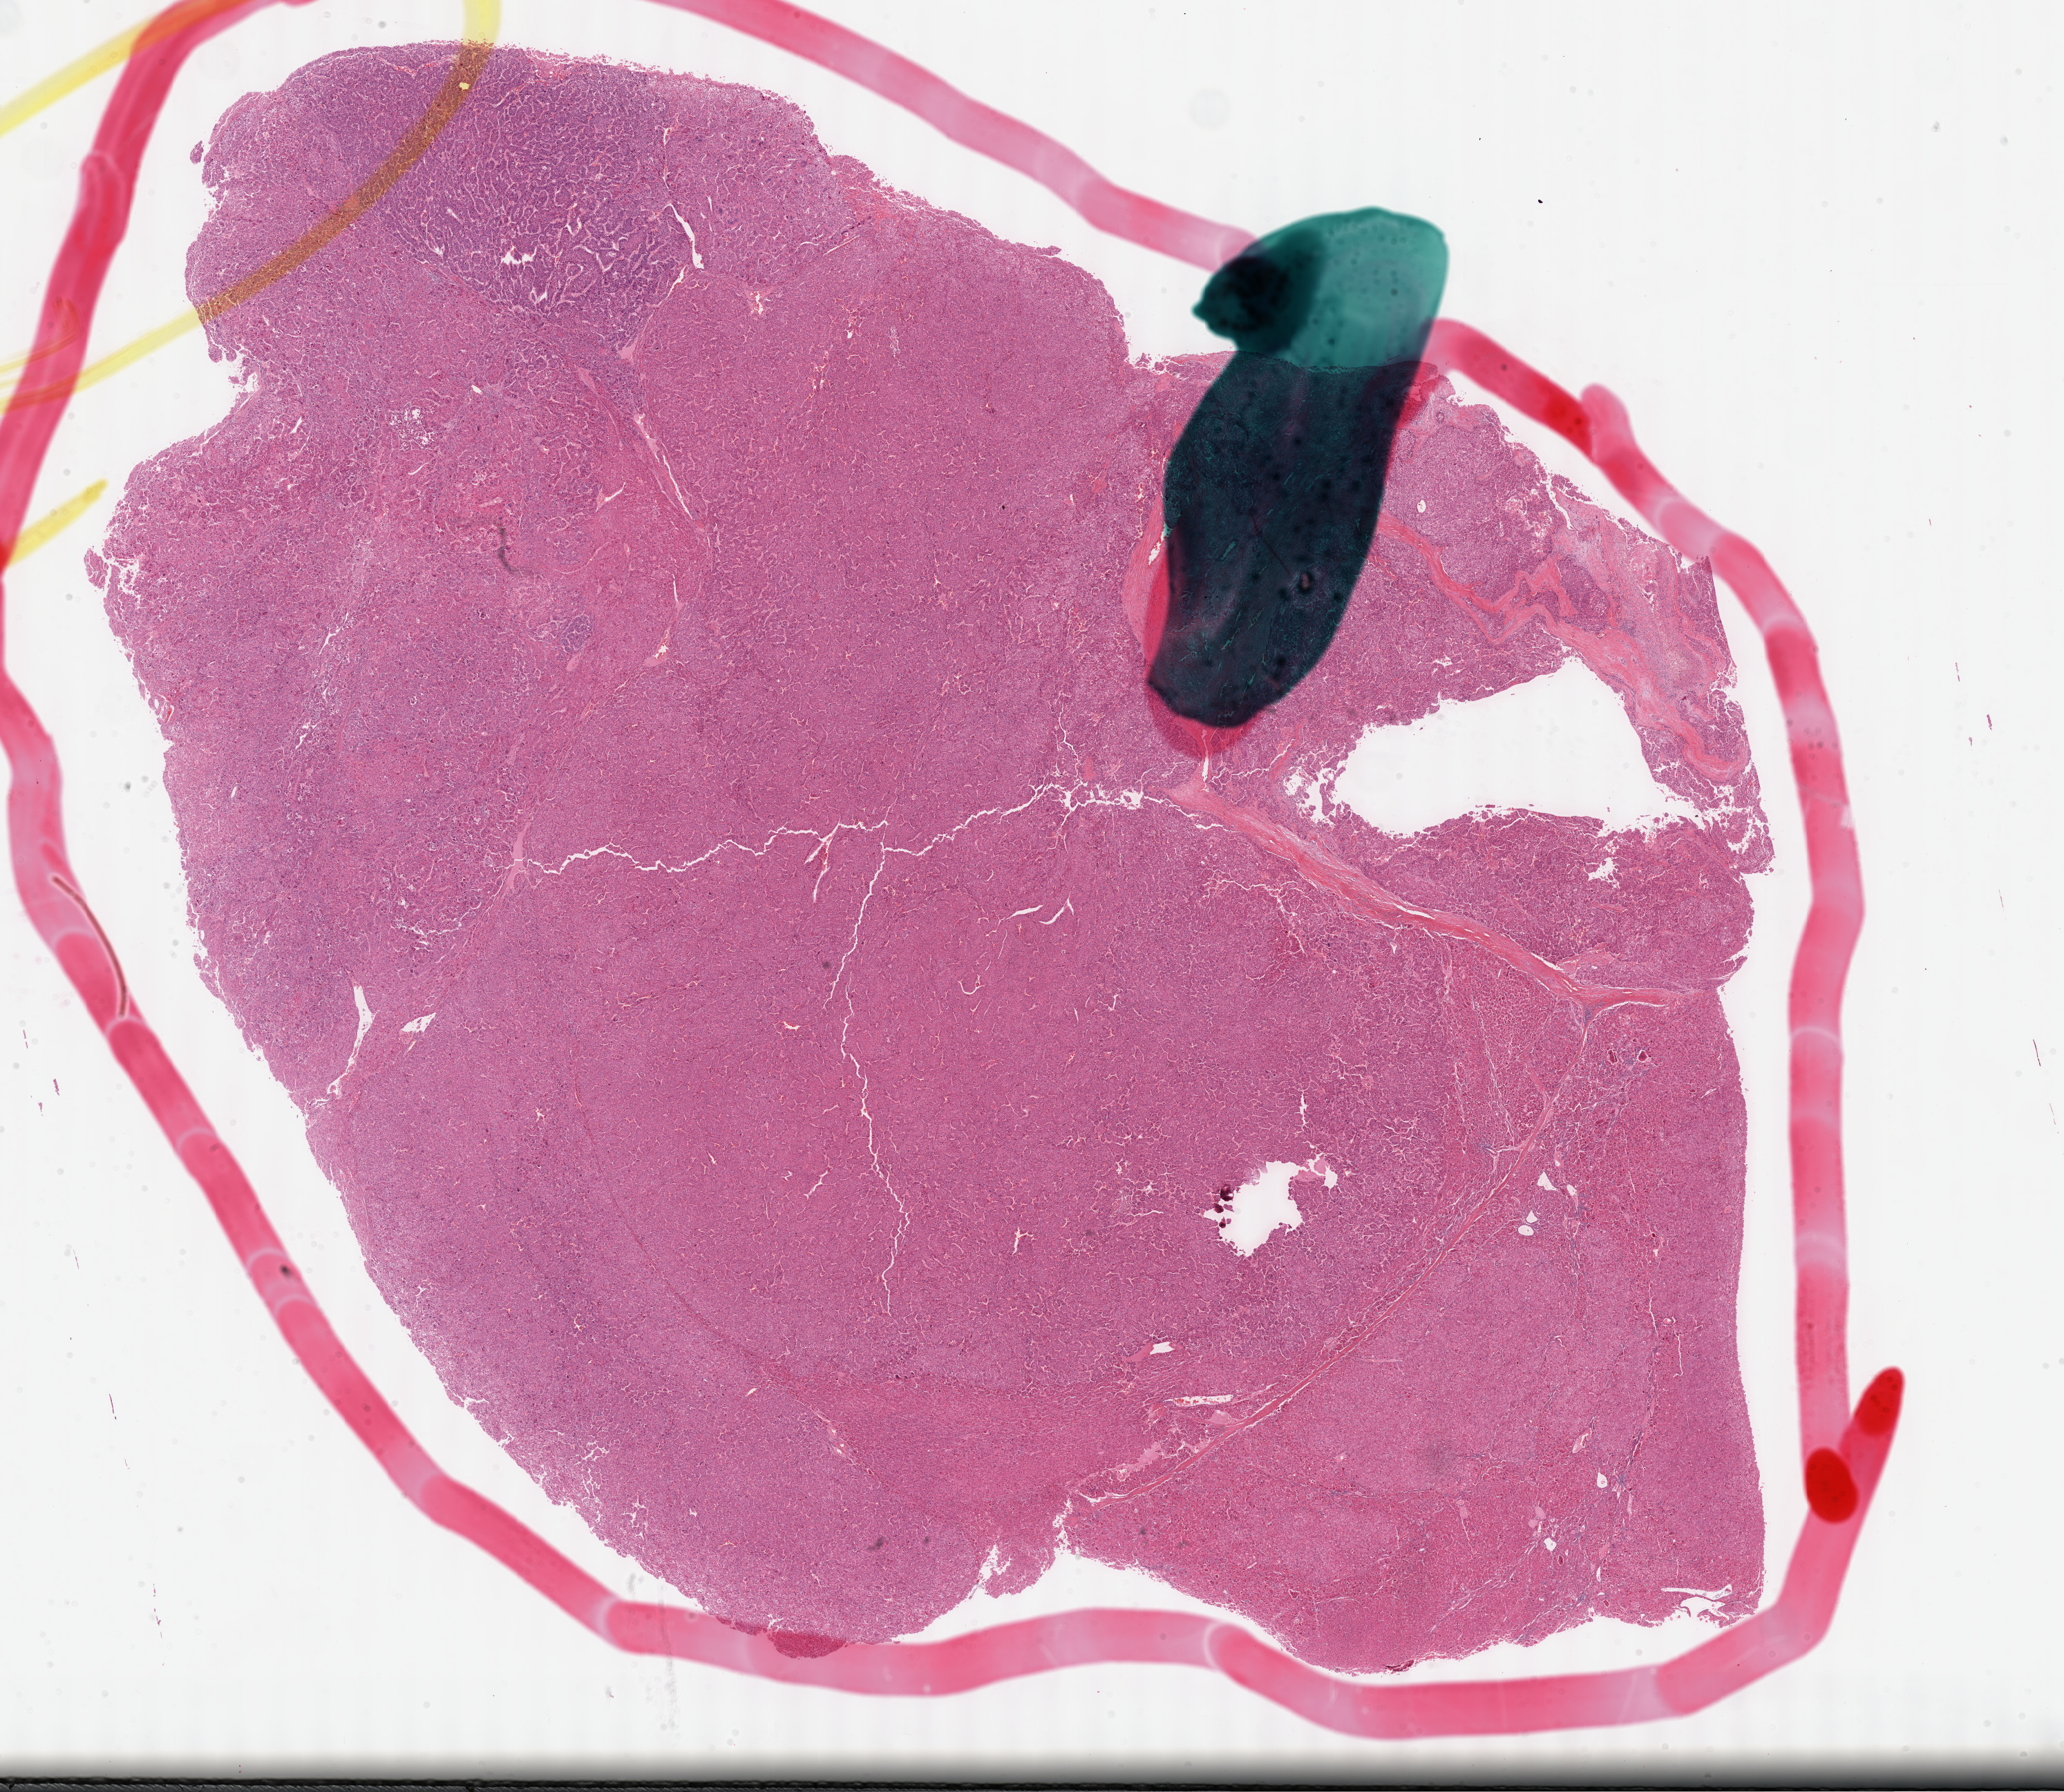
H&E whole-slide image — low-resolution overview of the scanned area, about 24.2 x 21.0 mm (slide scanned at 40x), FFPE section, liver, primary tumour sample. Female, age 53 years at initial diagnosis.
Pathologic diagnosis: Hepatocellular carcinoma, NOS.